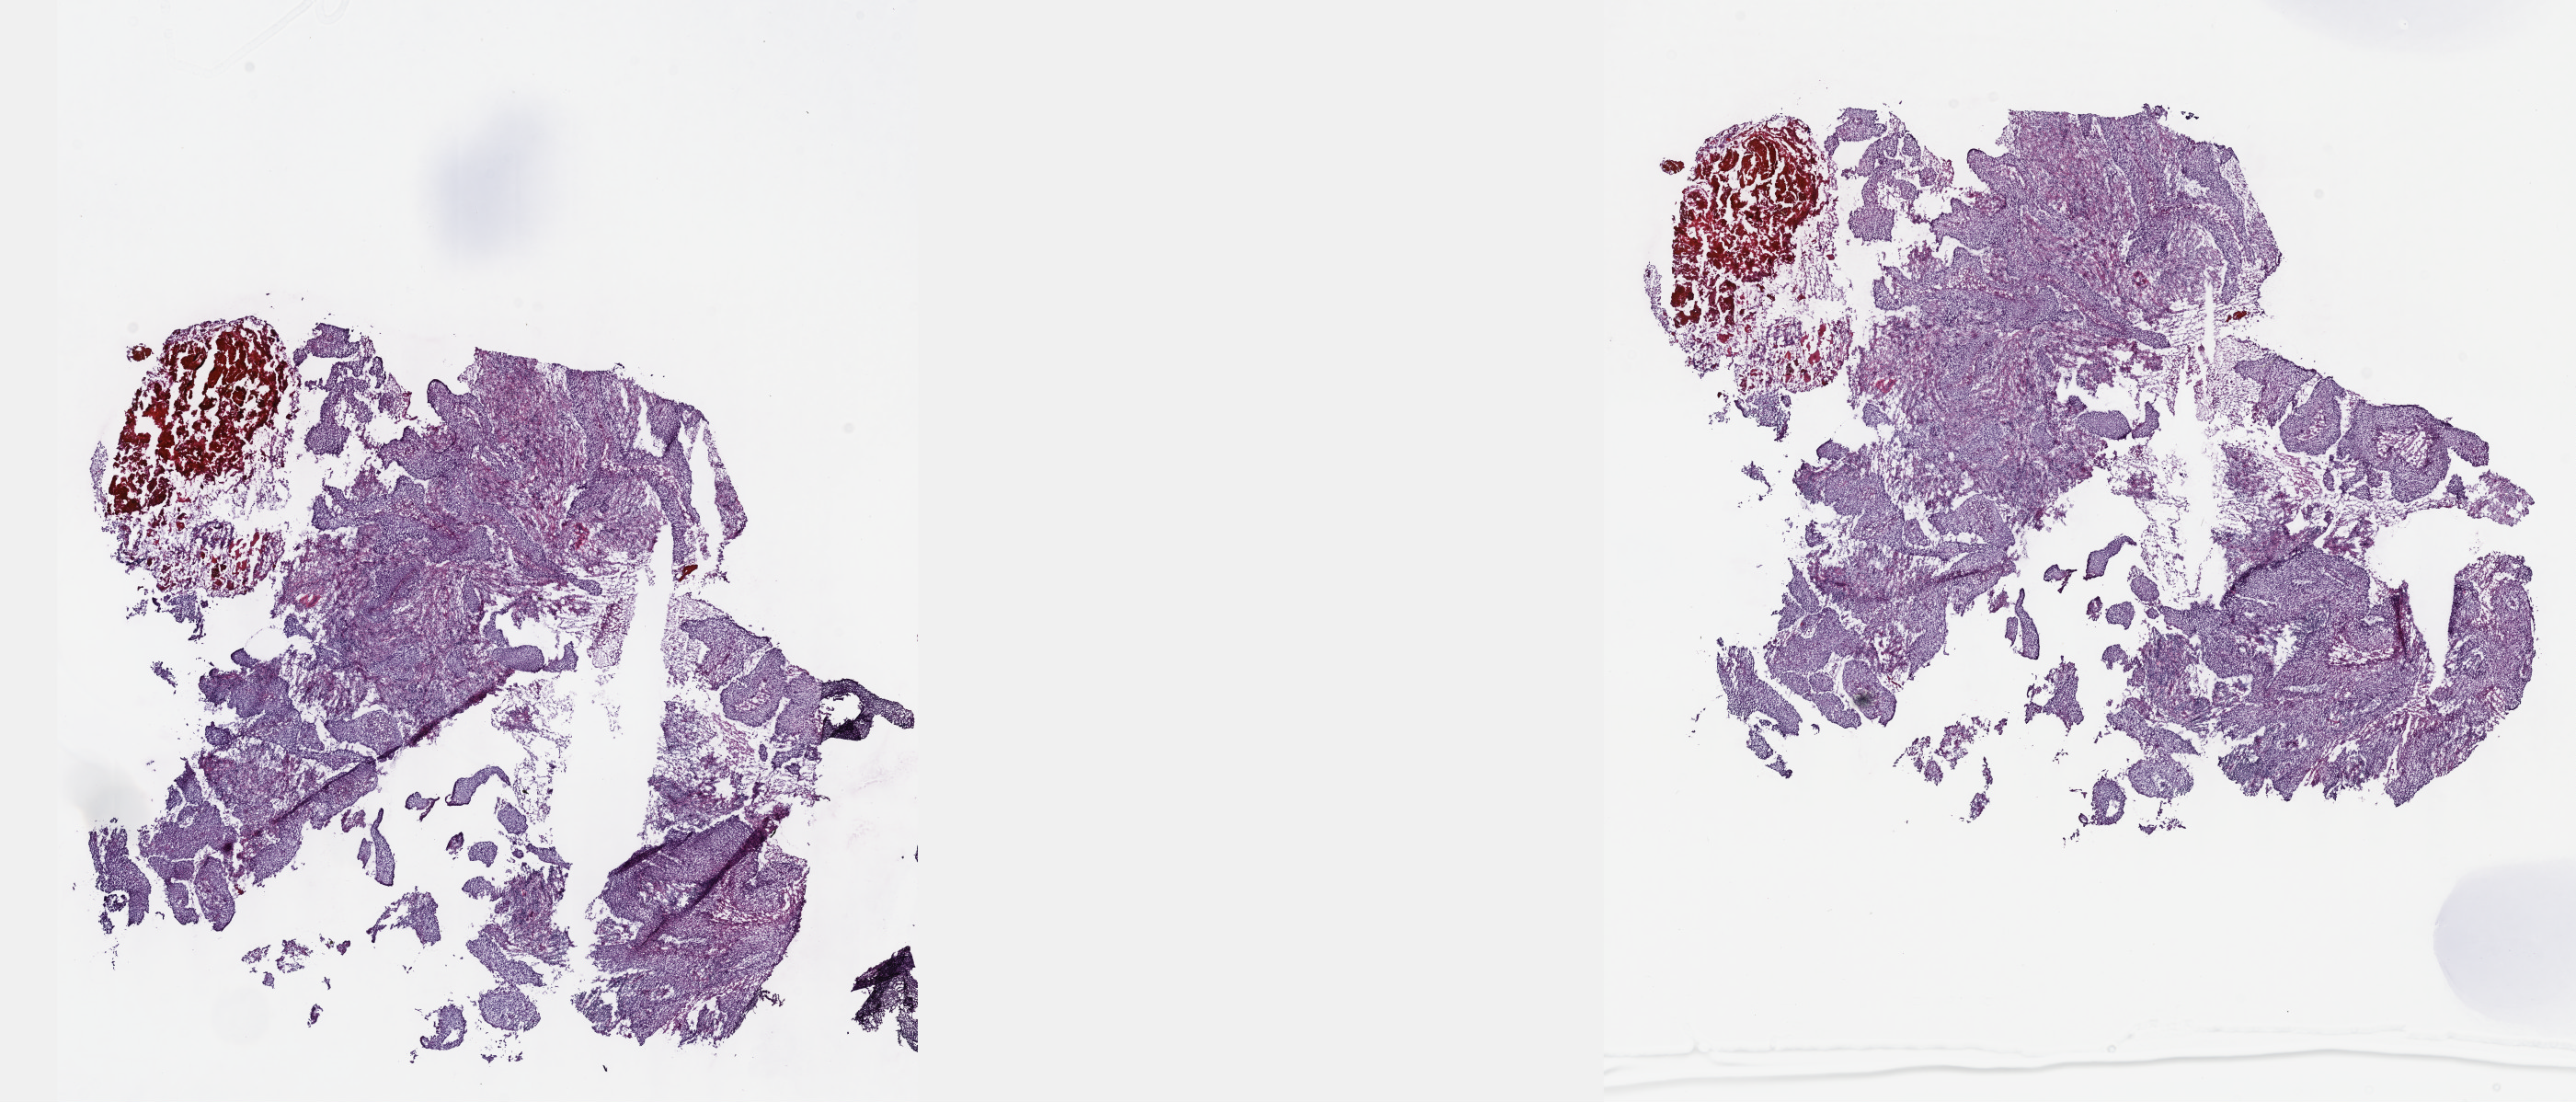
Whole-slide histology image, Hematoxylin and eosin (H&E) stained — shown as a low-resolution overview of the whole scanned area (about 22.6 x 9.7 mm, slide scanned at 40x), frozen section, primary tumour sample from the cervix. Female patient; age at initial diagnosis 58 years. Histologic grade: G2 (moderately differentiated). Pathologist review of this section (percent, as recorded): tumour cells 70%, tumour nuclei 70%, normal cells 0%, stromal cells 25%, necrosis 5%. Inflammatory infiltration, as recorded: lymphocyte infiltration 10%, monocyte infiltration 5%, neutrophil infiltration 5%.
* histologic diagnosis: Squamous cell carcinoma, large cell, nonkeratinizing, NOS
* FIGO stage: IIIB